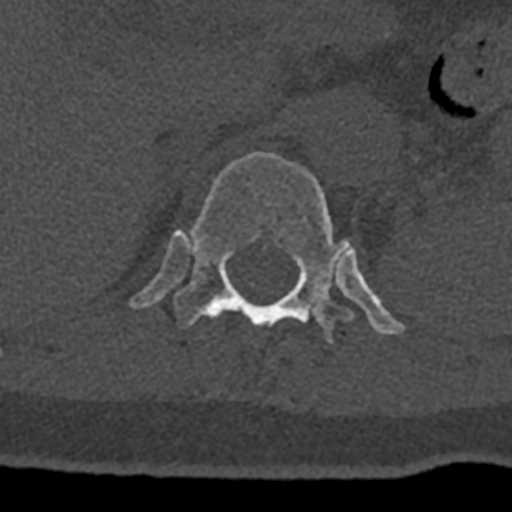
CT including the spine, one axial slice. Bone window (W 1800 / L 400 HU). 0.5 mm slice thickness. 512 × 512 image matrix, field of view 160 × 160 mm. Male patient, age 74 years. Case-level facts recorded for this patient, not image findings: primary cancer: renal.
Annotated regions visible in this slice (semi-automatic segmentation, software-assisted and operator-edited):
- T12 vertebra: bounding box [x1, y1, x2, y2] px = [128, 151, 407, 345]